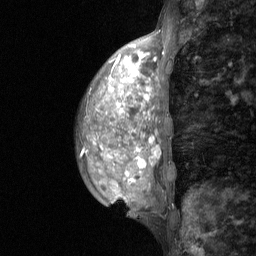
Breast MRI (dynamic contrast-enhanced), one sagittal slice. Slice 19 of 64 in the series (ordered by position). Dynamic contrast-enhanced study with each time point stored as its own series, time point 2 of 3 at this slice position (early post-contrast, ordered by acquisition time). 1.5 T. TE 4.8 ms, TR 27 ms. 2 mm slice thickness. 256 × 256 image matrix, field of view 200 × 200 mm. Female patient, age 36 years. From the clinical record (not read from this slice): setting: breast cancer imaged before/during neoadjuvant chemotherapy; receptor status: HR-positive, HER2-negative.
Structures marked on this image (semi-automatically segmented with operator editing):
- analysis volume of interest (the breast-tissue region the enhancement analysis was run in; not a lesion): bounding box (x1, y1, x2, y2) in pixels: (77, 96, 175, 210)
- tumour enhancement mask (voxels above the 90 % enhancement threshold inside the analysis volume of interest): (117, 104, 146, 167)